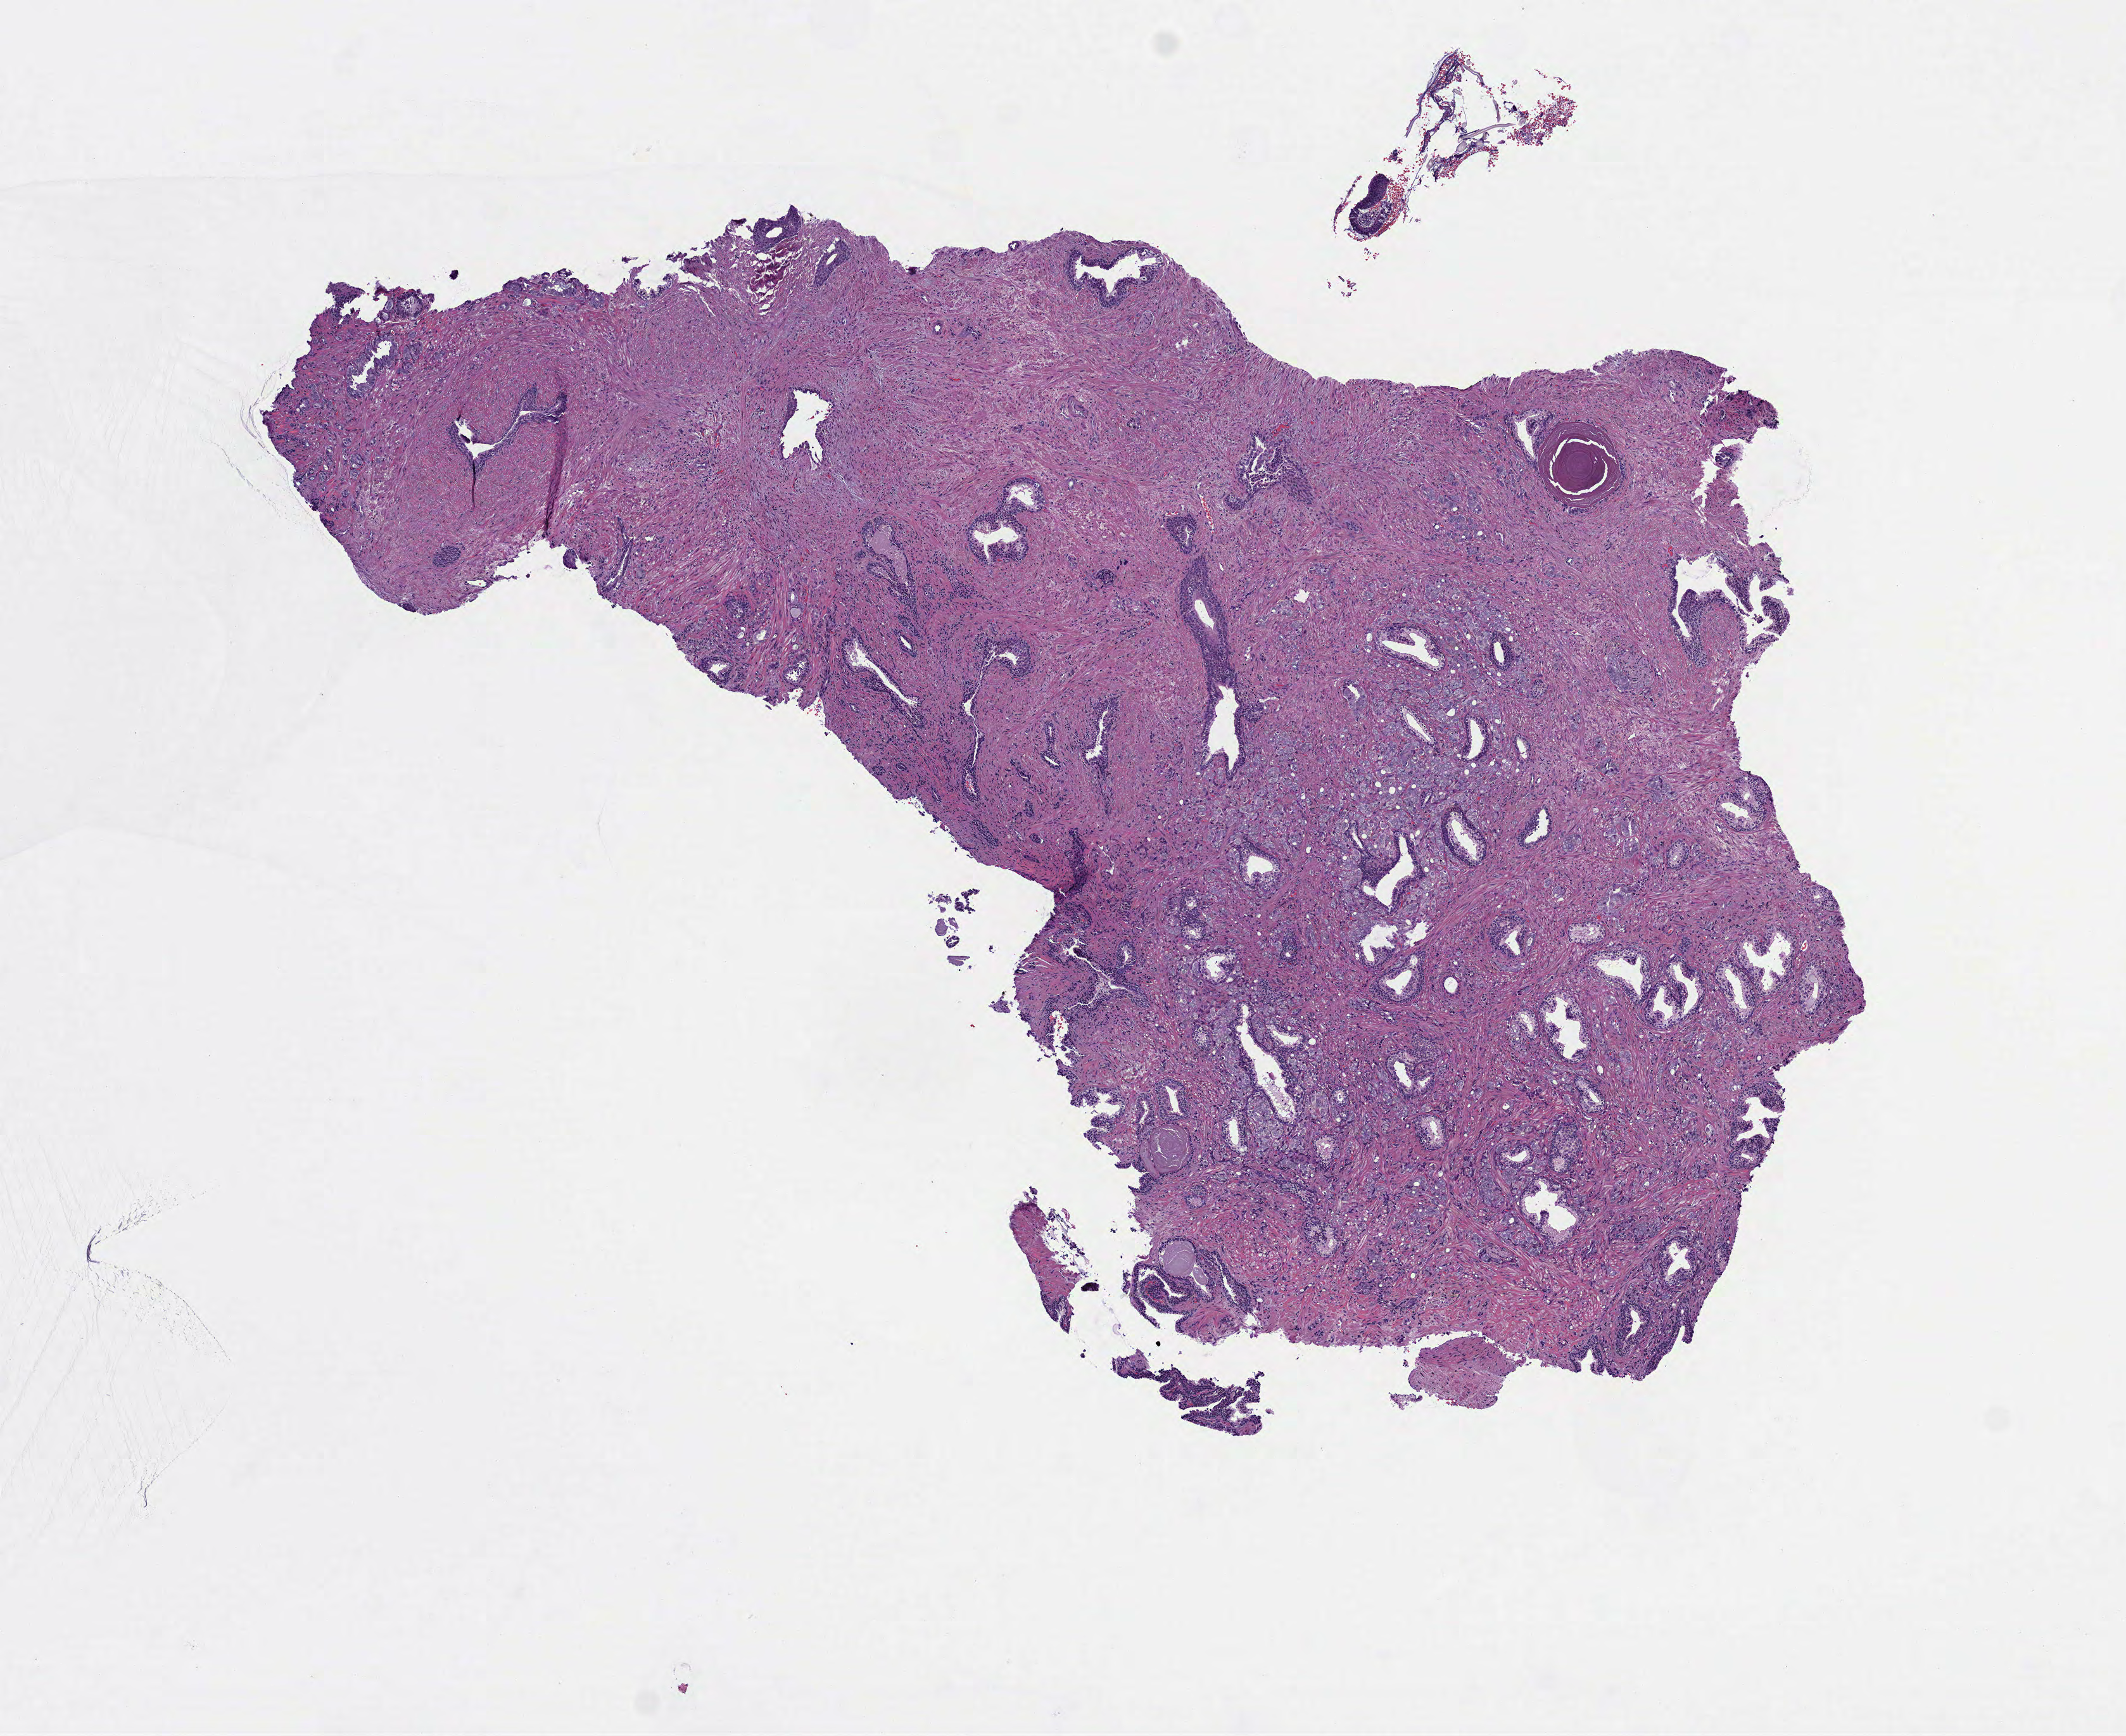
Hematoxylin and eosin (H&E) stained whole-slide image — low-resolution overview of the scanned area, about 6.8 x 5.5 mm (from a 40x scan), formalin-fixed paraffin-embedded (FFPE) diagnostic section, prostate, primary tumour sample. Patient: male, age at initial diagnosis 55 years. Gleason score: 7 (4+3).
Histologic diagnosis: Adenocarcinoma, NOS (prostate gland).